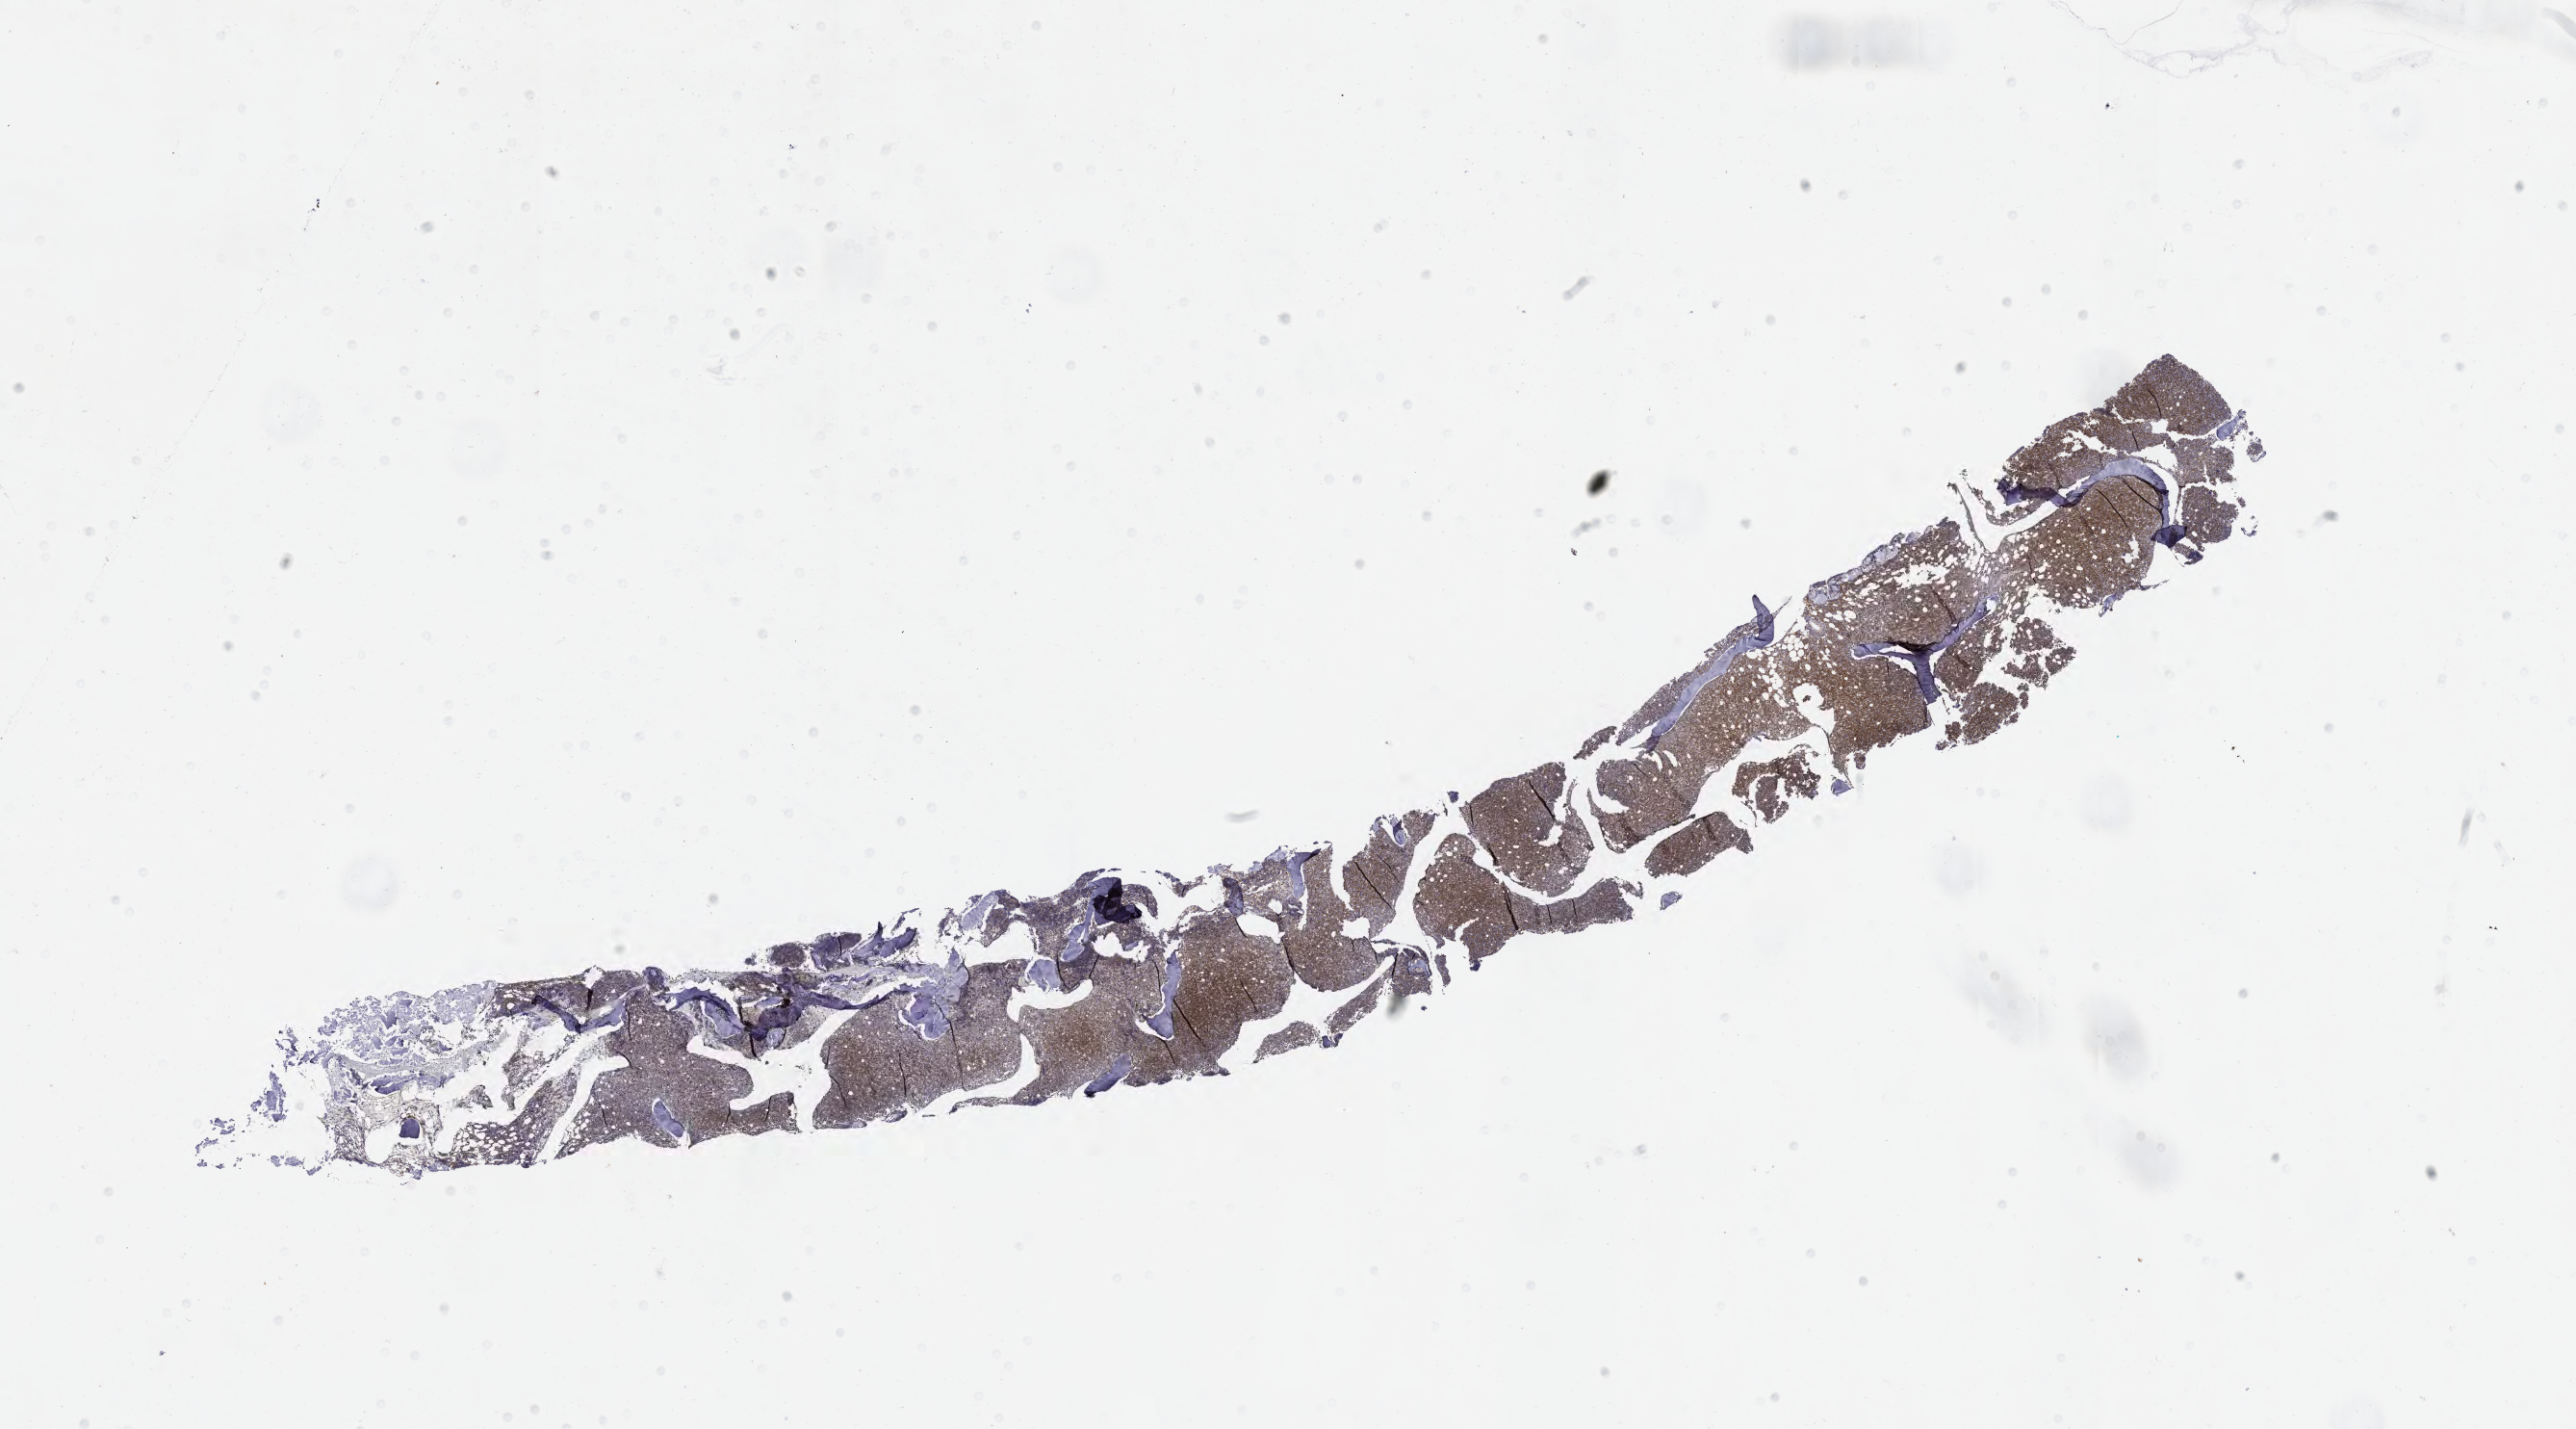
IHC for BCL2, whole-slide image, shown as a low-resolution overview of the whole scanned area (about 21.6 x 12.0 mm); specimen: tumor tissue. Patient sex: male.
Histologic diagnosis: Burkitt lymphoma, NOS.